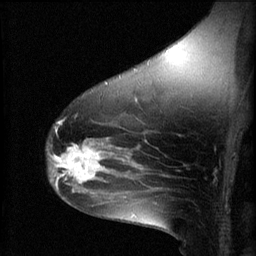
Breast MRI (dynamic contrast-enhanced), one sagittal slice. Slice 40 of 60 in the series (ordered by position). 3 images stored at this slice position (order not interpretable as contrast timing). 1.5 T. TE 4.2 ms, TR 8.2 ms. 2 mm slice thickness. 256 × 256 image matrix, field of view 180 × 180 mm. Patient: female, 49 years.
Annotated regions visible in this slice (semi-automatically segmented with operator editing):
- analysis volume of interest (the breast-tissue region the enhancement analysis was run in; not a lesion): bounding box [x1, y1, x2, y2] px = [47, 136, 109, 187]
- tumour enhancement mask (voxels above the 70 % enhancement threshold inside the analysis volume of interest): [49, 140, 109, 187]